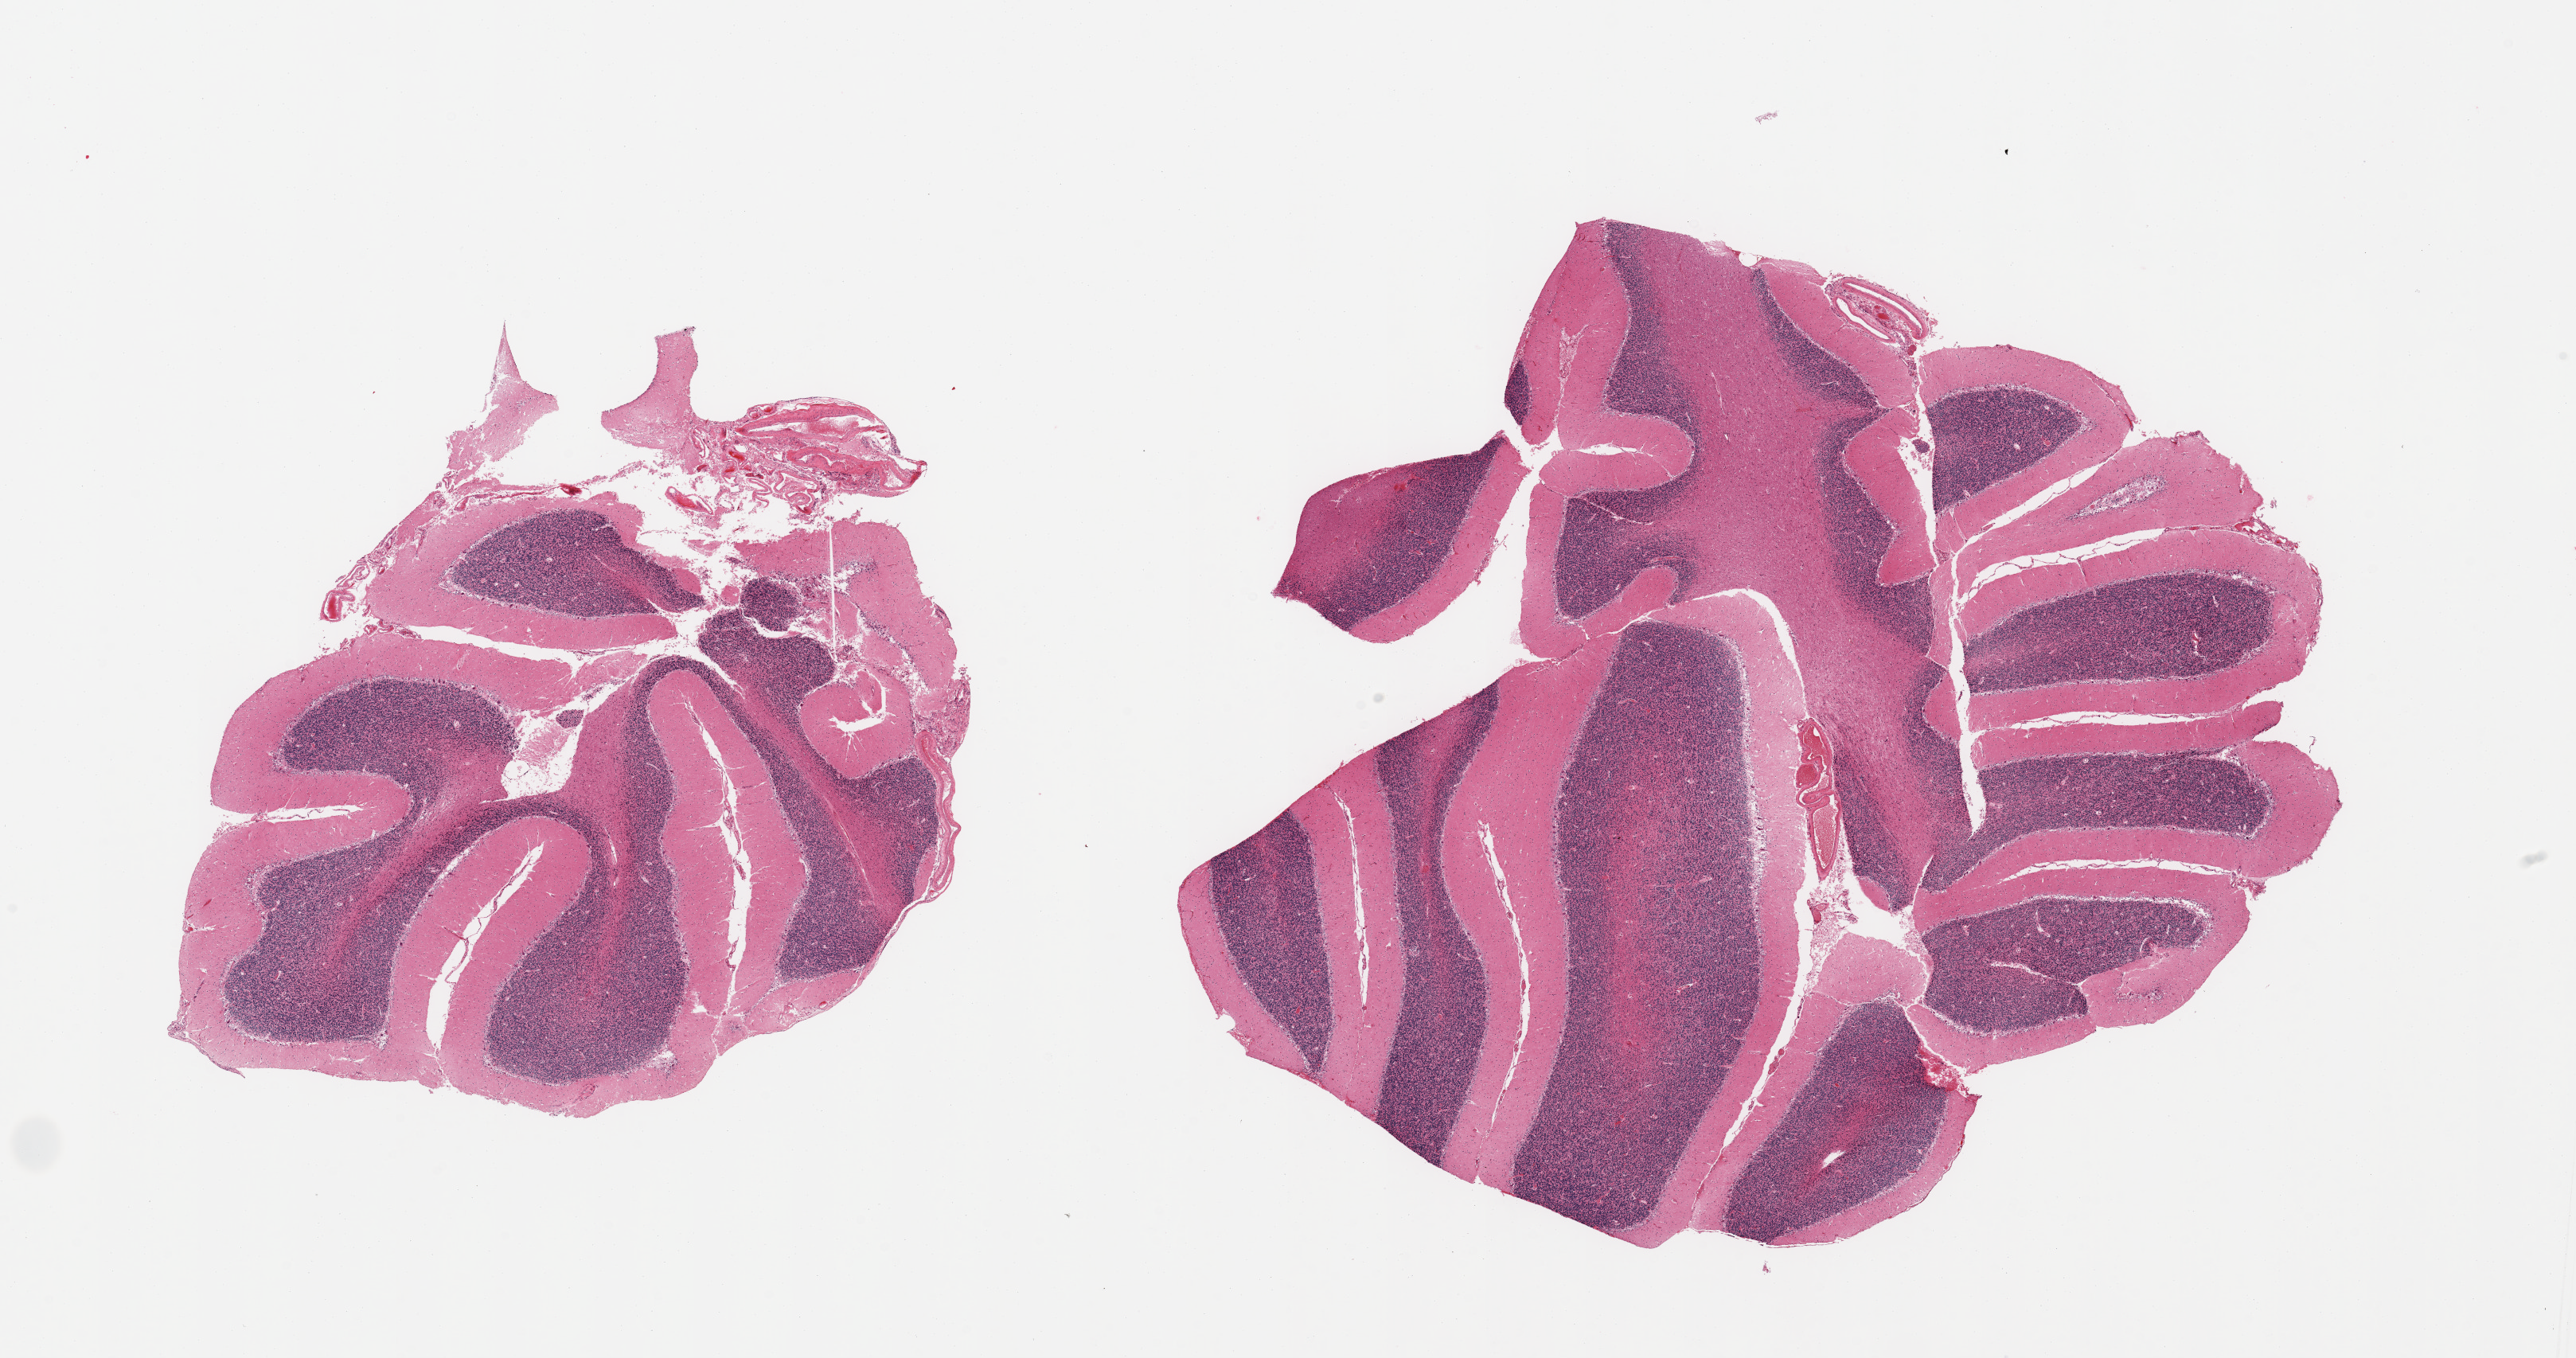
Digitized hematoxylin and eosin (H&E)-stained section — a low-resolution overview of the entire scanned area, about 25.6 x 13.5 mm; PAXgene-fixed, paraffin-embedded tissue; section of cerebellum (target tissue); tissue donor sample. Donor: male.
* reviewer comment on this tissue sample: 2 pieces, no abnormalities